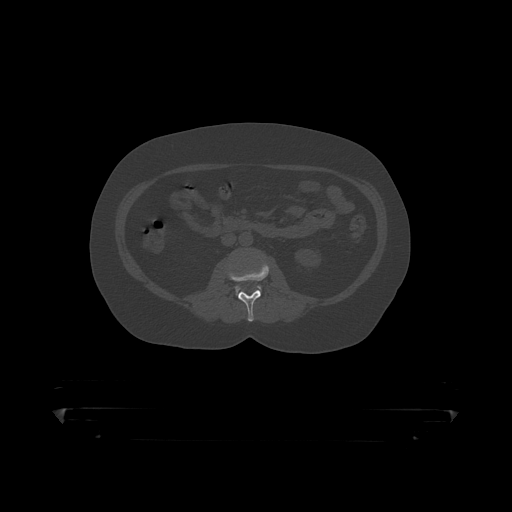
CT including the spine, one axial slice; position 108 of 390 along the scan axis; reconstruction kernel STANDARD; bone window (W 1800 / L 400 HU); 1.25 mm slice thickness; 512 × 512 image matrix, field of view 650 × 650 mm. Patient: male, 60 years. Case-level facts recorded for this patient, not image findings: primary cancer: prostate.
Structures marked on this image (semi-automatically segmented with operator editing):
- L2 vertebra: bounding box [x1, y1, x2, y2] px = [228, 260, 270, 319]
- L3 vertebra: [236, 286, 261, 292]